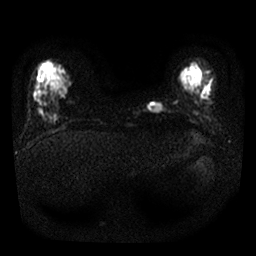
Breast MRI, one axial slice. Slice 4 of 24 in the series (ordered by position). Diffusion-weighted series; image 2 of 4 stored at this slice position (different b-values; order by instance number). 1.5 T. 4 mm slice thickness. 256 × 256 image matrix, field of view 300 × 300 mm. Female patient.
Structures marked on this image (expert manual segmentation):
- tumour on diffusion-weighted imaging: bounding box [x1, y1, x2, y2] px = [148, 102, 163, 113]